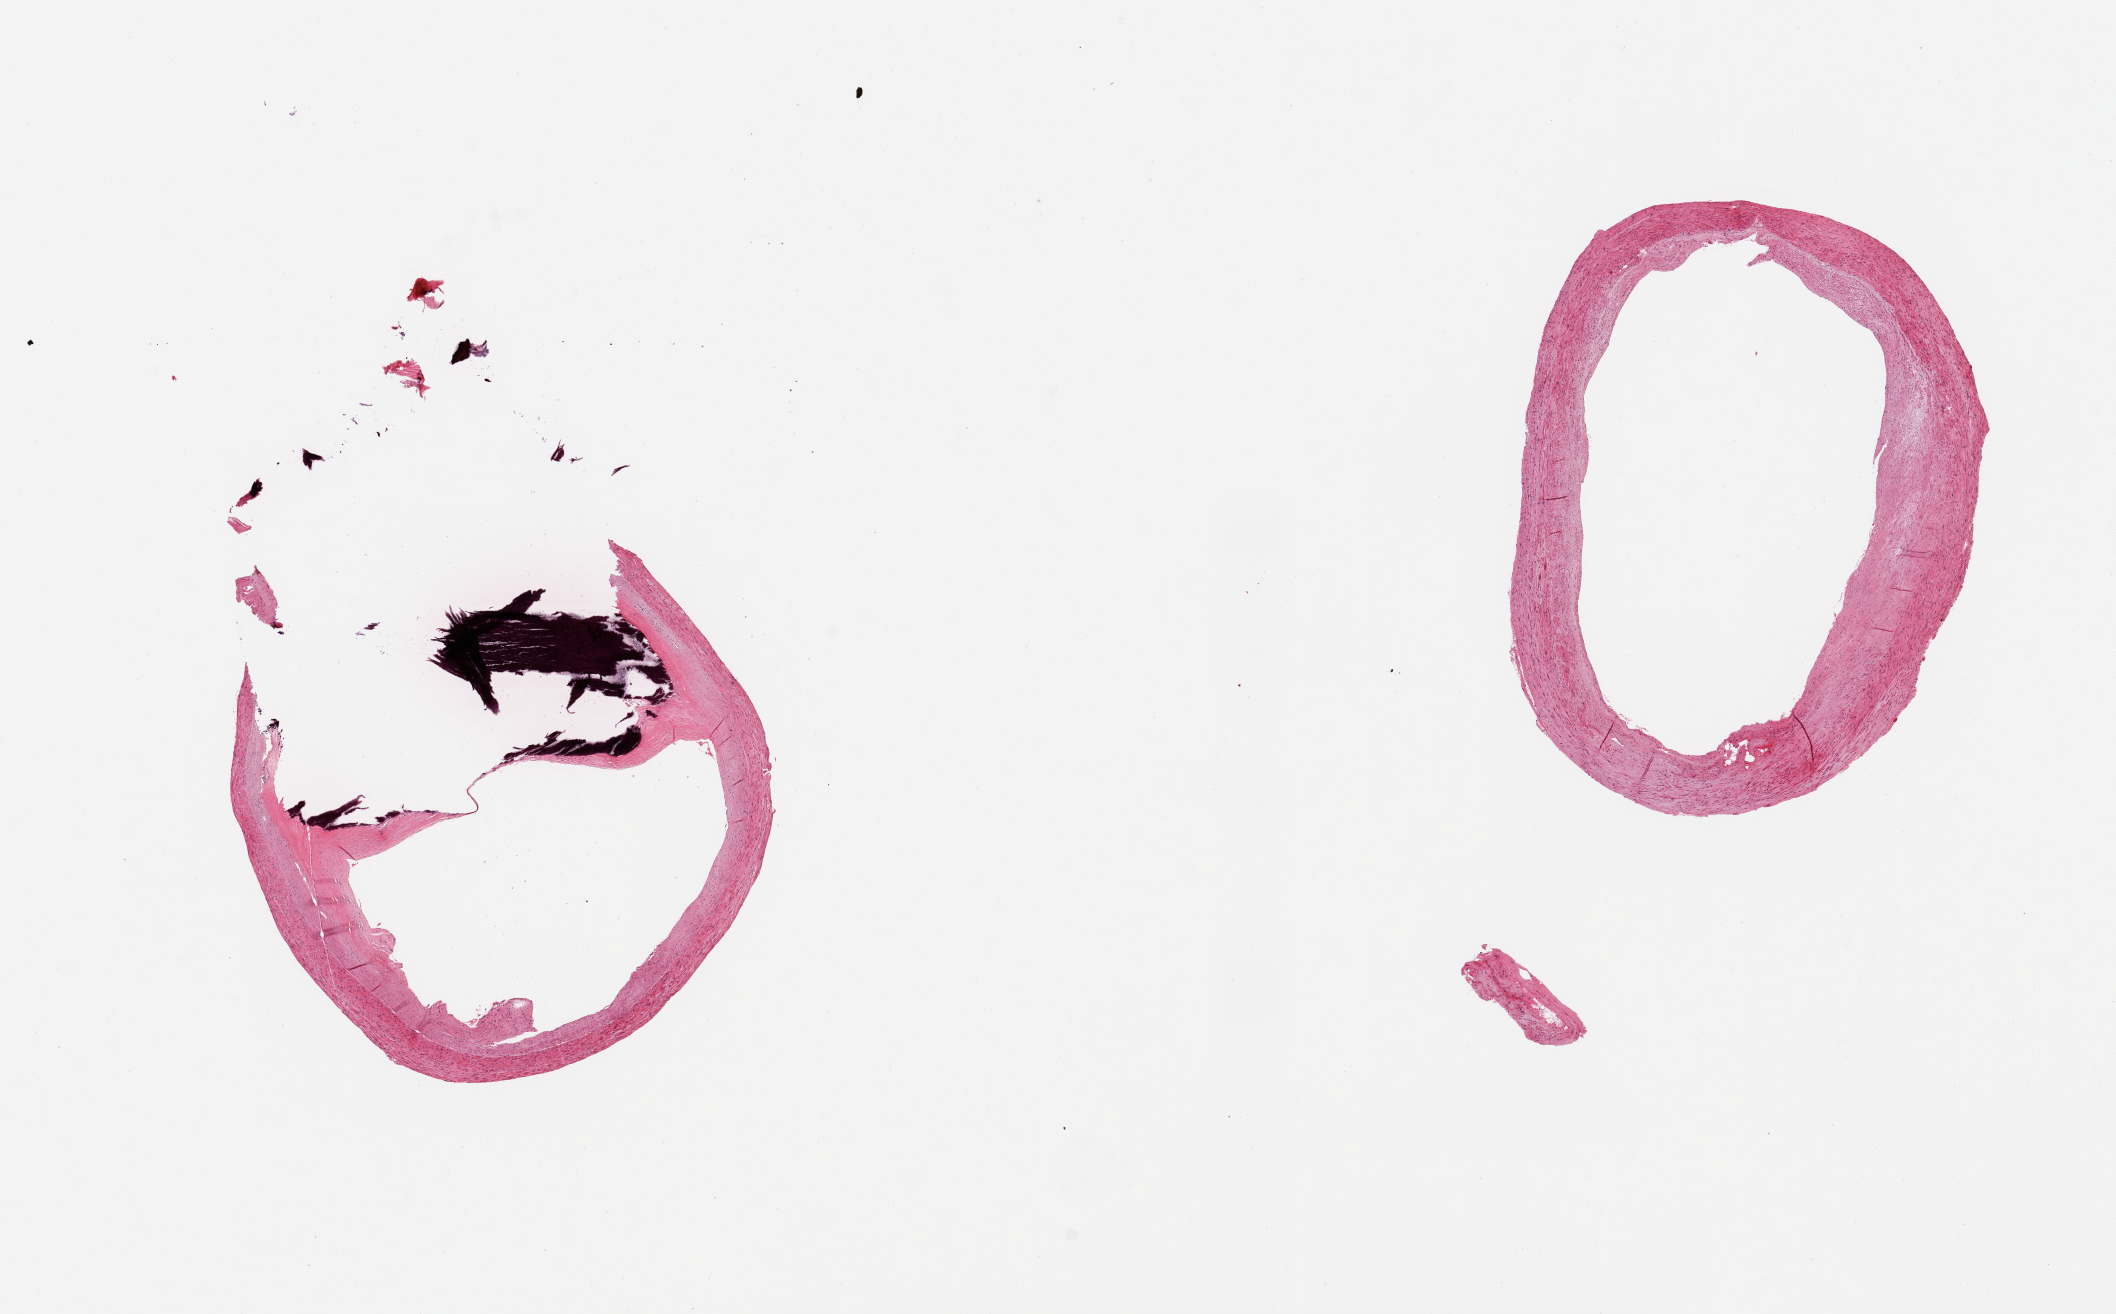
Hematoxylin and eosin (H&E) whole-slide image, brightfield, whole scanned area (about 16.7 x 10.4 mm, acquisition: 20x scan) shown as a low-resolution overview; PAXgene-fixed paraffin-embedded (PFPE) section; section of coronary artery (target tissue); donor tissue sample.
Pathologist's review note for this sample: 2 pieces, 50 occlusive calcified atherosis.